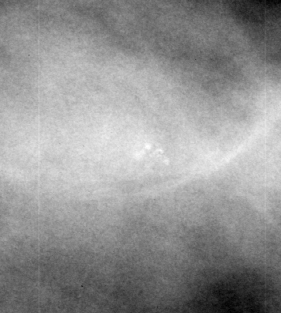
Crop from a digitized film mammogram around one marked abnormality, left breast, CC view, BI-RADS breast density category 3 (scale 1–4).
Calcifications, morphology pleomorphic, distribution clustered; BI-RADS assessment category 4; subtlety rating 3 on a 1 (subtle) to 5 (obvious) scale; pathology (as recorded): benign.